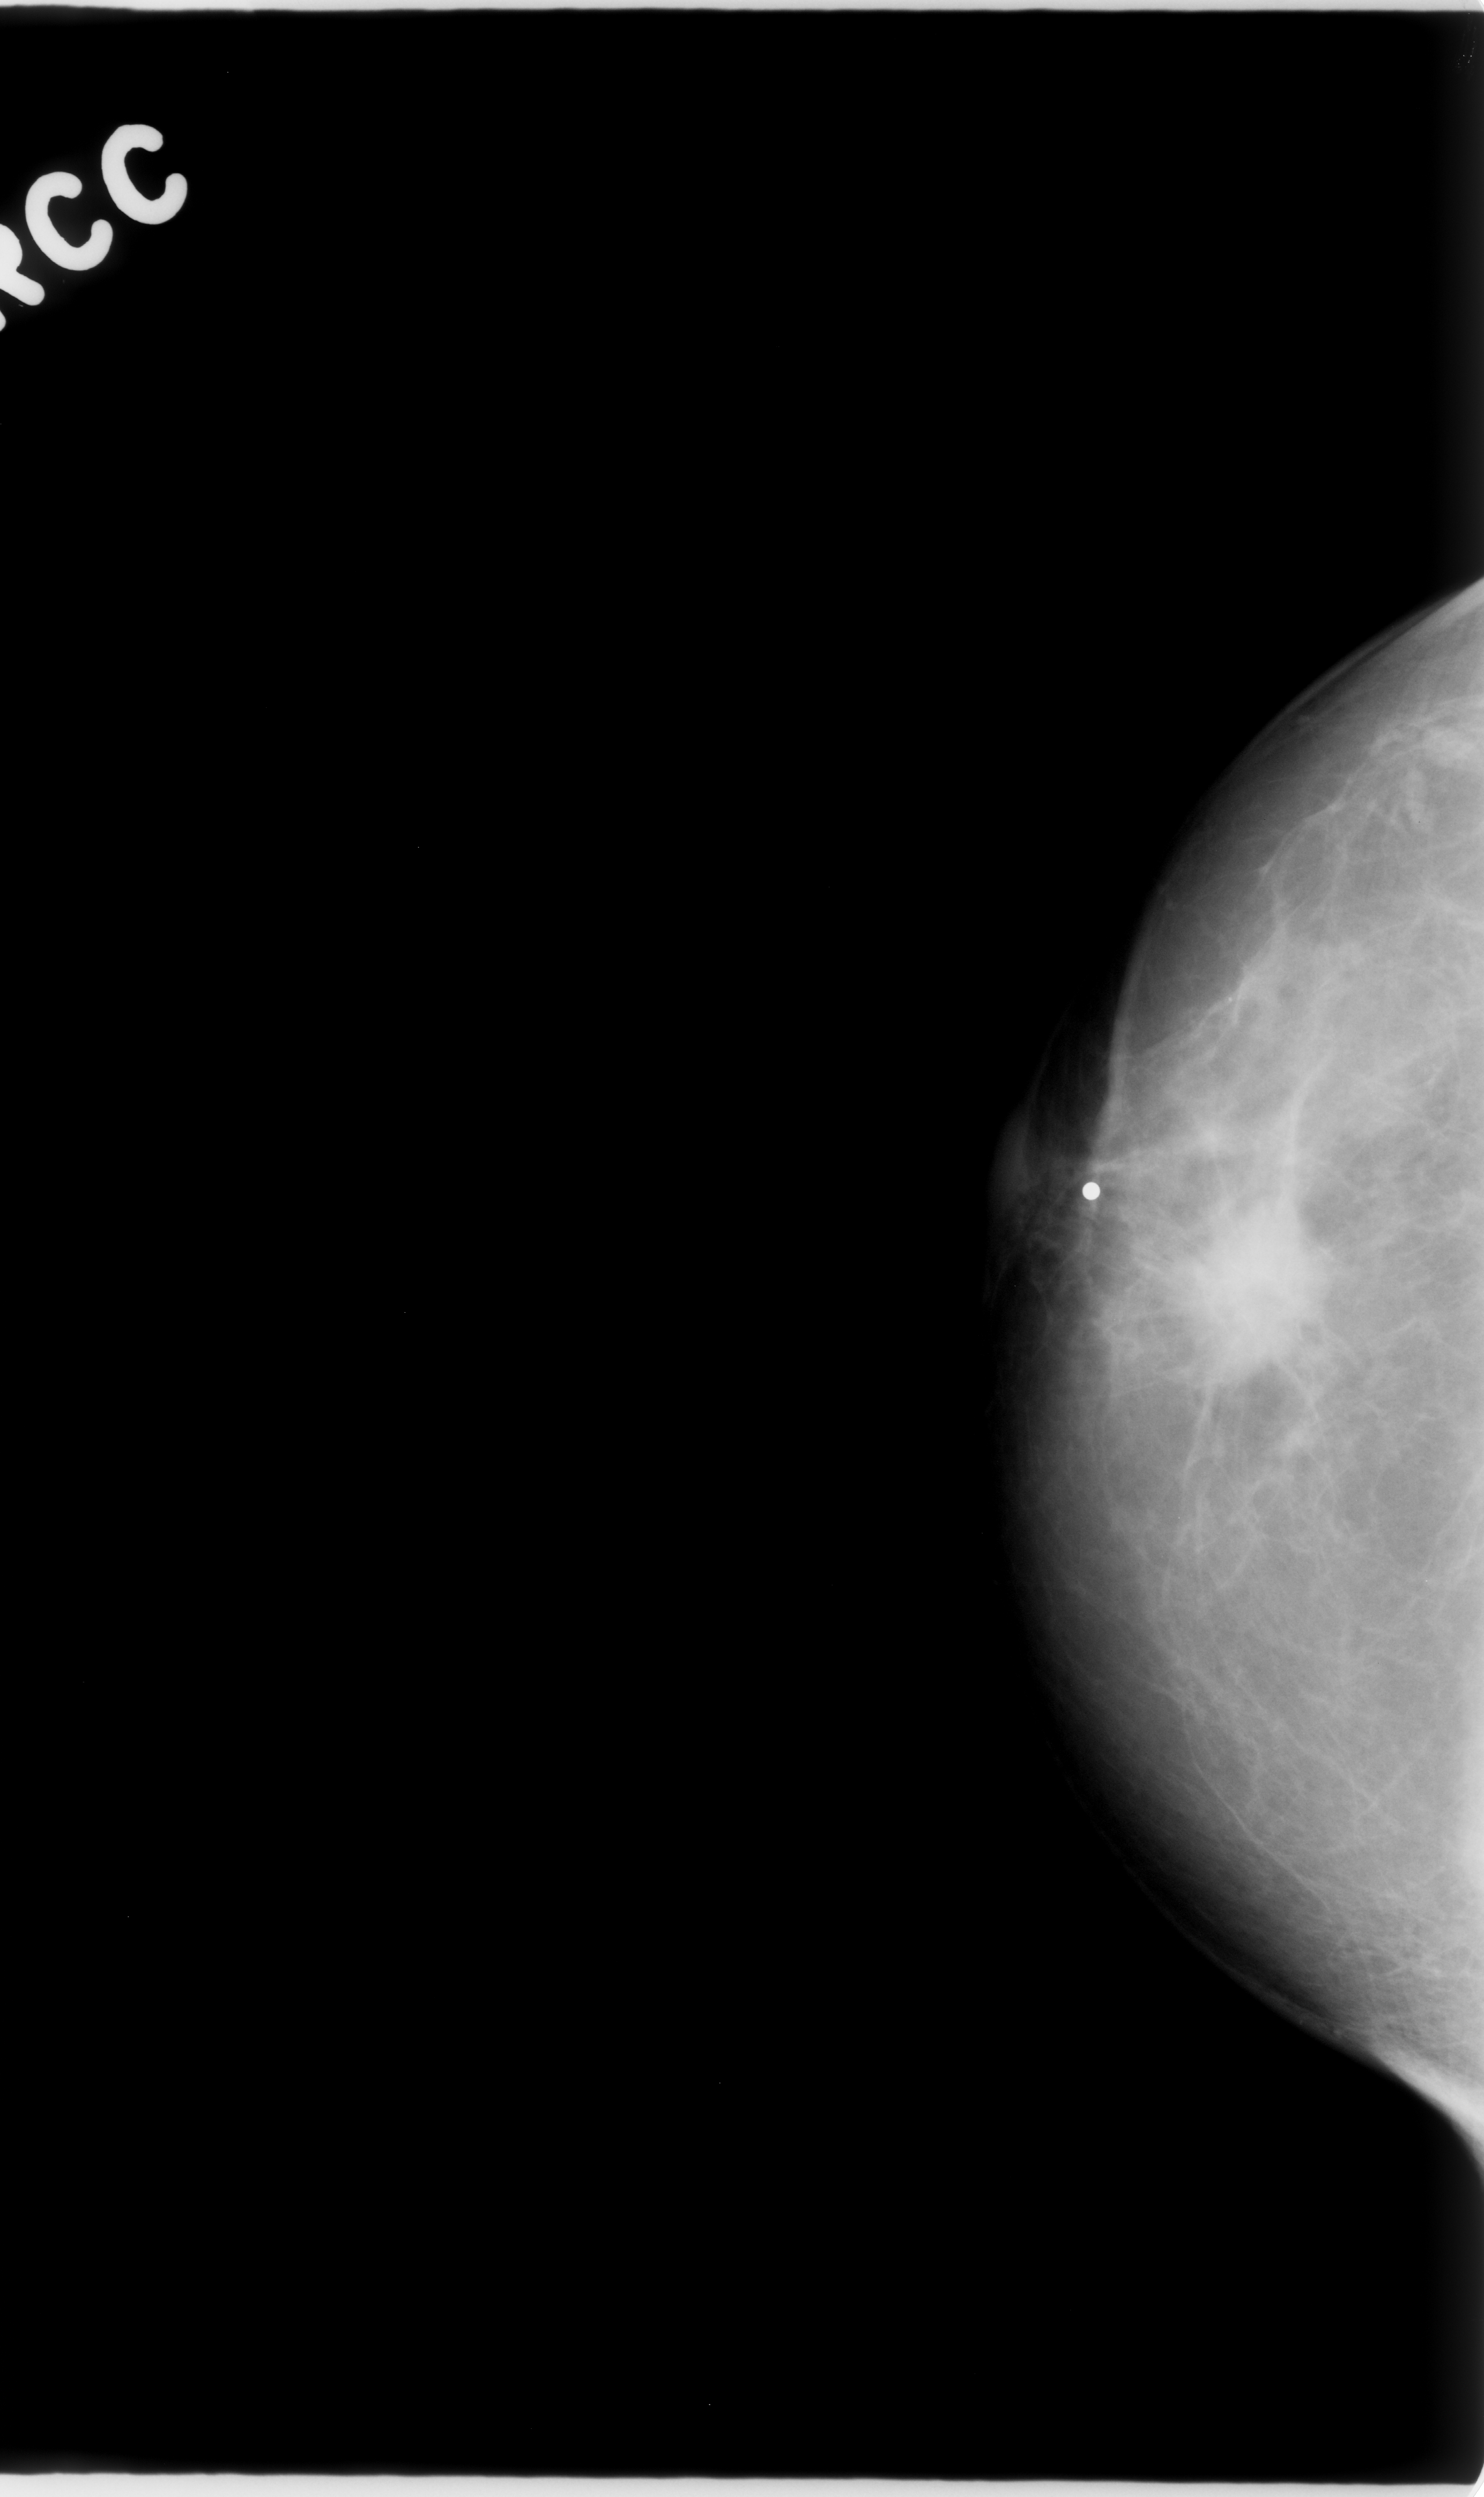
Scanned film-screen mammogram. Right breast. Craniocaudal (CC) view. BI-RADS breast density category 1 (scale 1–4). 1484 × 2497 image matrix.
Marked abnormalities (boxes around the expert regions of interest):
- mass, shape irregular, margins spiculated; BI-RADS assessment category 5; pathology (as recorded): malignant: bounding box [x1, y1, x2, y2] px = [1191, 1203, 1315, 1387]